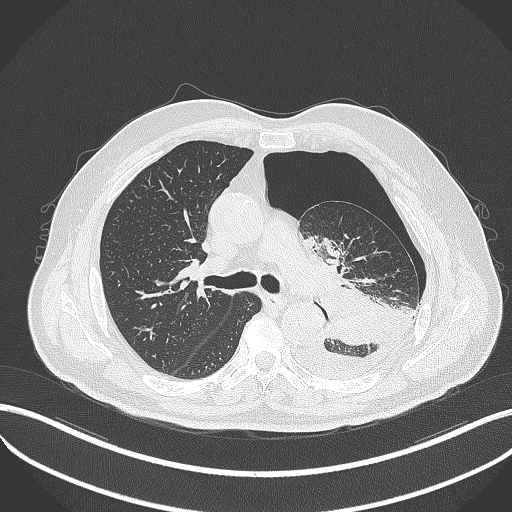
Chest CT, one axial slice; position 328 of 464 along the scan axis; lung window (W 1500 / L -600 HU); 1 mm slice thickness; 512 × 512 image matrix, field of view 400 × 400 mm. Male patient, age 76 years. From the clinical record (not read from this slice): clinical TNM (as recorded): T3 N0 M1b.
Annotated regions visible in this slice (bounding box drawn by a radiologist):
- lung tumour (recorded histology: adenocarcinoma): box from (x=315, y=287) to (x=399, y=346) px